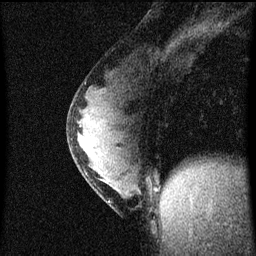
Breast MRI (dynamic contrast-enhanced), one sagittal slice. Position 29 of 60 along the scan axis. Dynamic contrast-enhanced series, image 2 of 4 at this slice position (ordered by acquisition). 1.5 T. TE 4.2 ms, TR 8 ms. 256 × 256 image matrix. Patient: female, 33 years.
Annotated regions visible in this slice (semi-automatically segmented with operator editing):
- analysis volume of interest (the breast-tissue region the enhancement analysis was run in; not a lesion): bounding box [x1, y1, x2, y2] px = [68, 76, 152, 215]
- tumour enhancement mask (voxels above the 70 % enhancement threshold inside the analysis volume of interest): [78, 124, 109, 203]